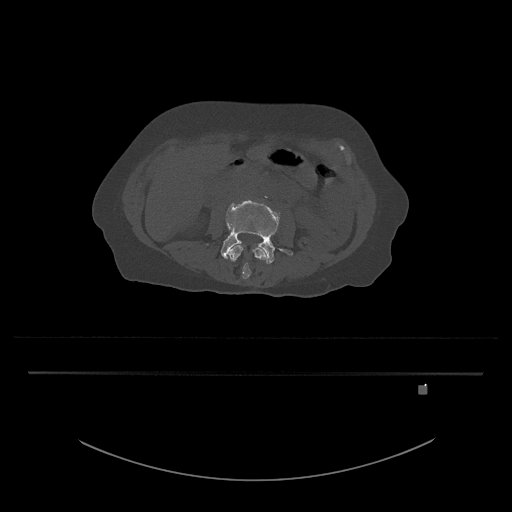
CT including the spine, one axial slice. Slice 388 of 797 in the series (ordered by position). Reconstruction kernel Br40s/3. Bone window (W 1800 / L 400 HU). 0.5 mm slice thickness. 512 × 512 image matrix. Patient: female, 57 years. From the clinical record (not read from this slice): primary cancer: cervical.
Annotated regions visible in this slice (semi-automatically segmented with operator editing):
- L3 vertebra: box from (x=229, y=245) to (x=268, y=279) px
- L4 vertebra: (x=206, y=200)–(x=293, y=264)